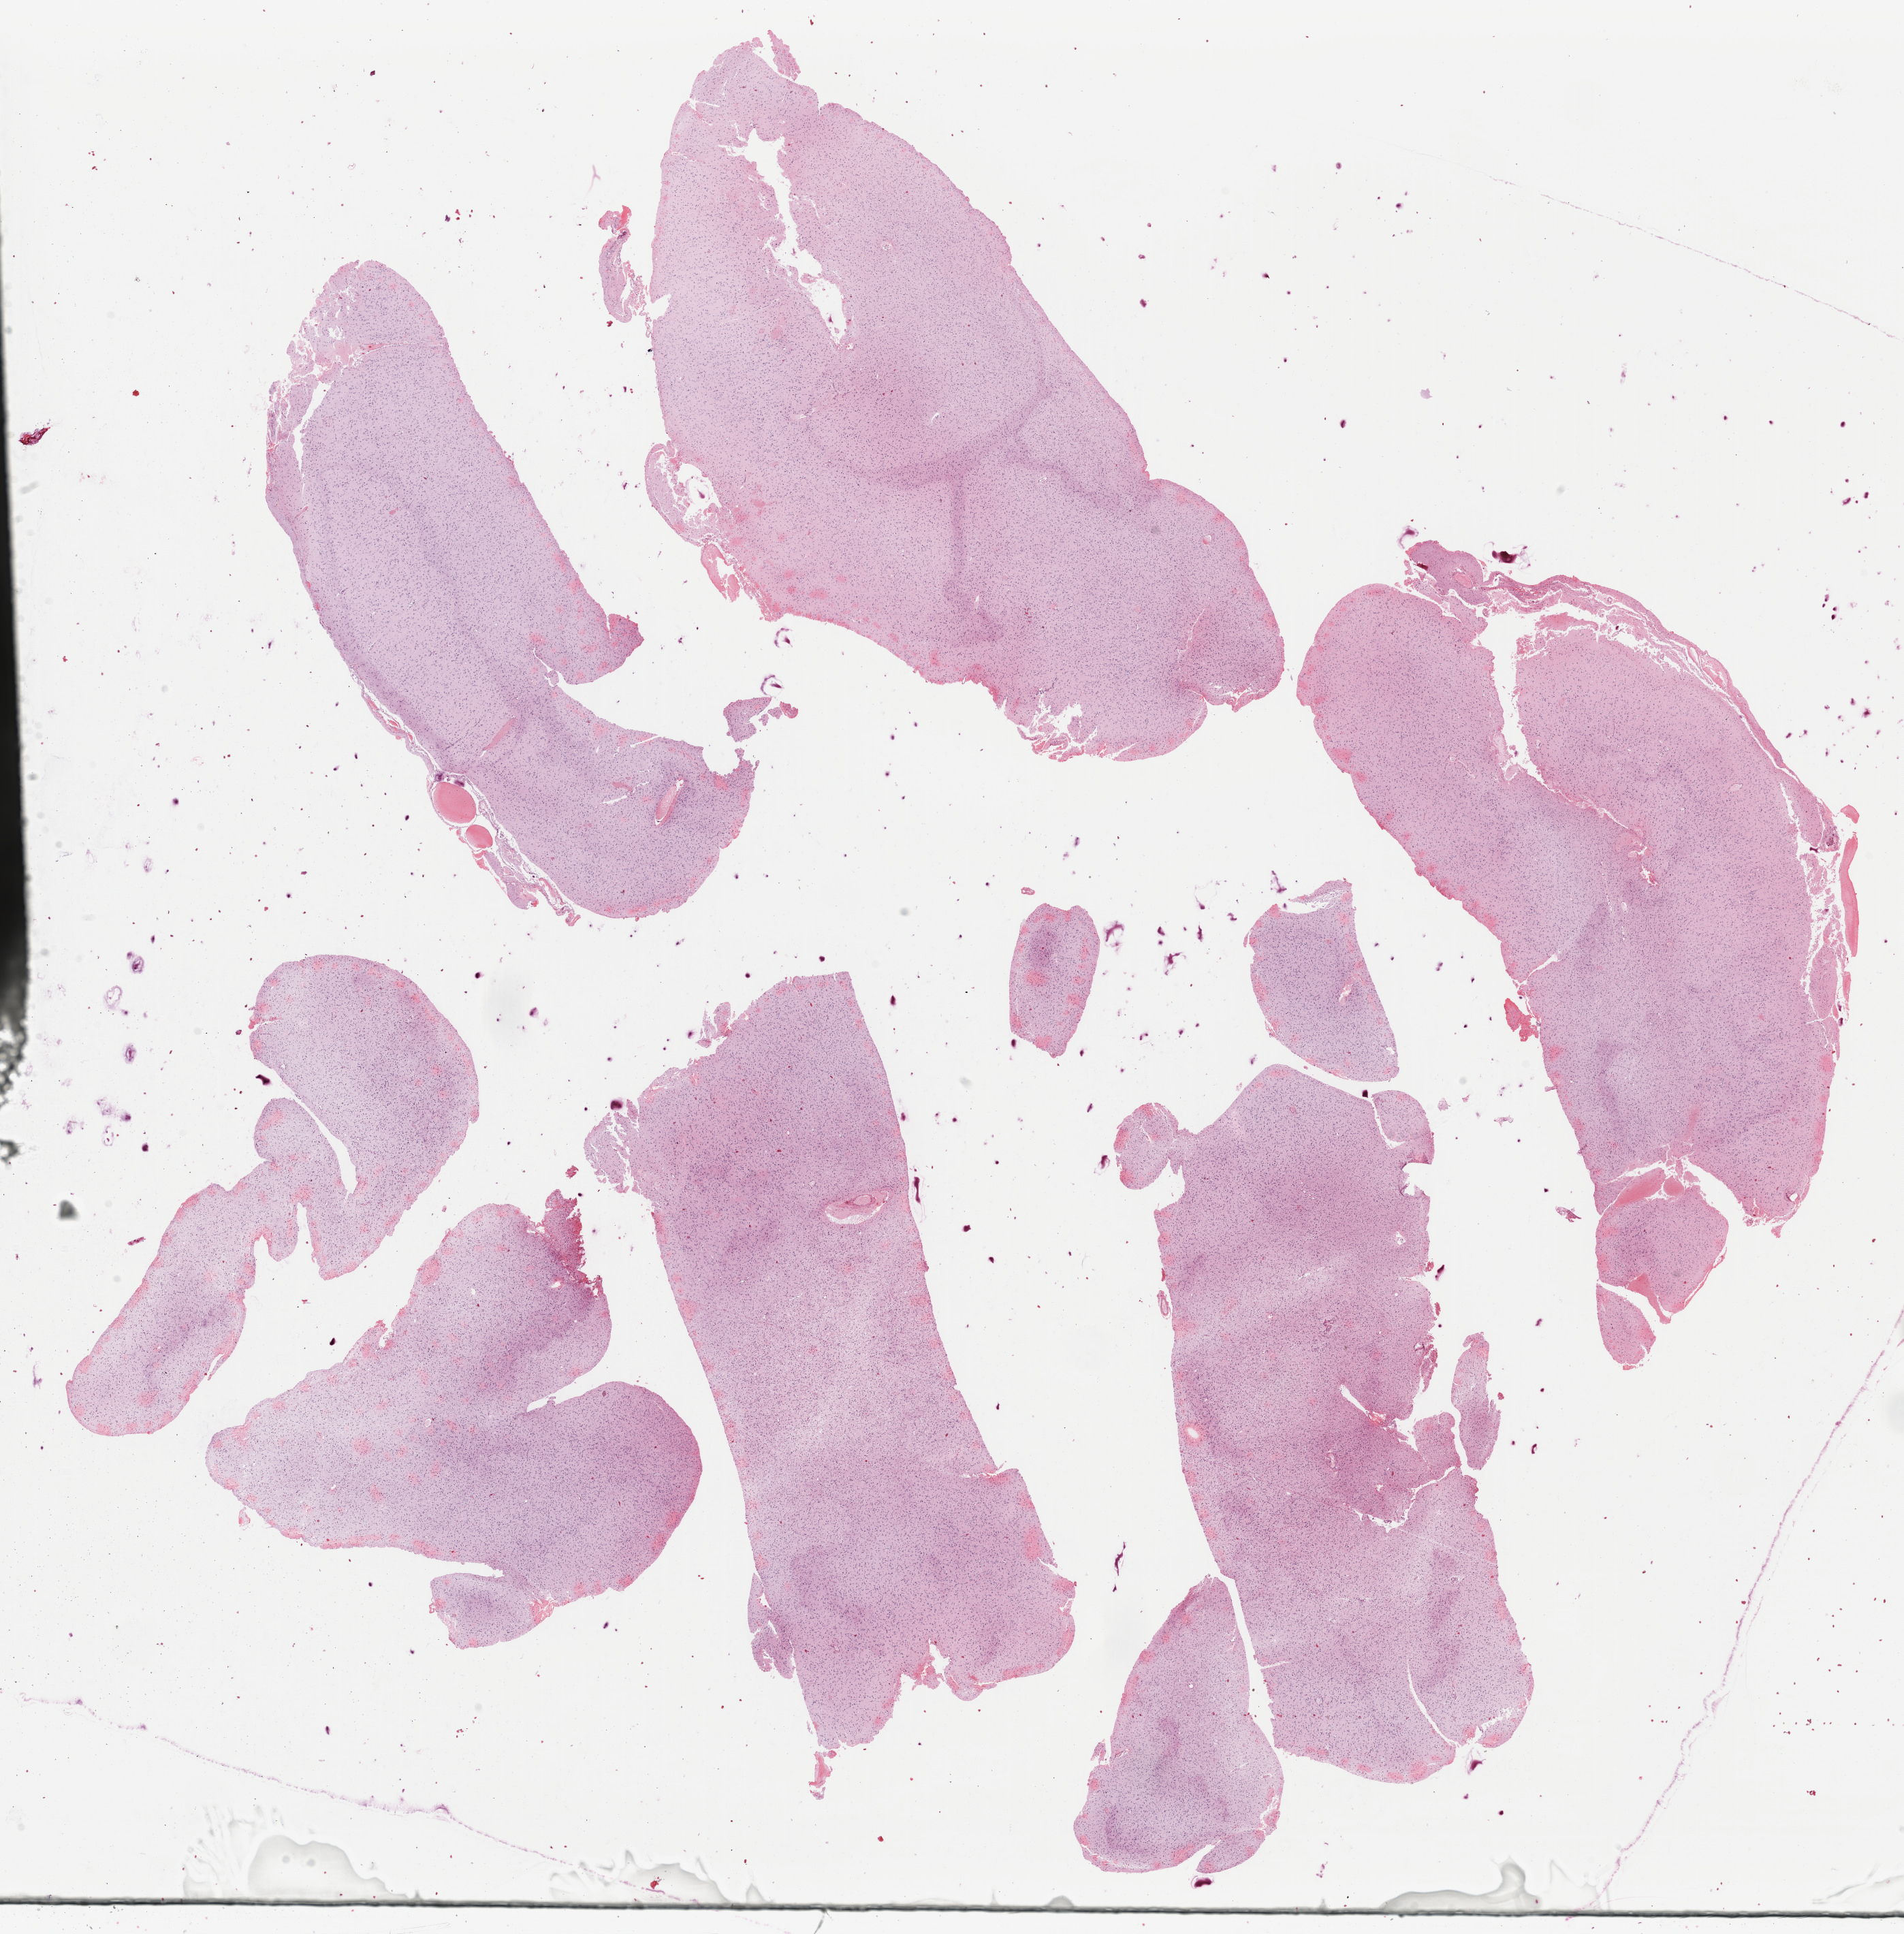
Digitized Hematoxylin and eosin (H&E) stained tissue section (whole slide) — shown as a low-resolution overview of the whole scanned area (about 22.1 x 22.4 mm), formalin-fixed paraffin-embedded (FFPE) diagnostic section, brain, primary tumour sample. Patient: female, age at initial diagnosis 32 years.
Diagnosis: Mixed glioma.